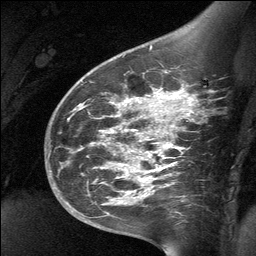
Breast MRI (dynamic contrast-enhanced), one sagittal slice; position 43 of 64 along the scan axis; dynamic contrast-enhanced study with each time point stored as its own series, time point 2 of 3 at this slice position (early post-contrast, ordered by acquisition time); 1.5 T; TE 4.8 ms, TR 27 ms; 2 mm slice thickness; 256 × 256 image matrix, field of view 200 × 200 mm. Patient: female, 39 years. From the clinical record (not read from this slice): setting: breast cancer imaged before/during neoadjuvant chemotherapy; receptor status: HER2-positive.
Structures marked on this image (semi-automatic segmentation, software-assisted and operator-edited):
- analysis volume of interest (the breast-tissue region the enhancement analysis was run in; not a lesion): bounding box (x1, y1, x2, y2) in pixels: (70, 69, 201, 224)
- tumour enhancement mask (voxels above the 90 % enhancement threshold inside the analysis volume of interest): (125, 93, 189, 179)